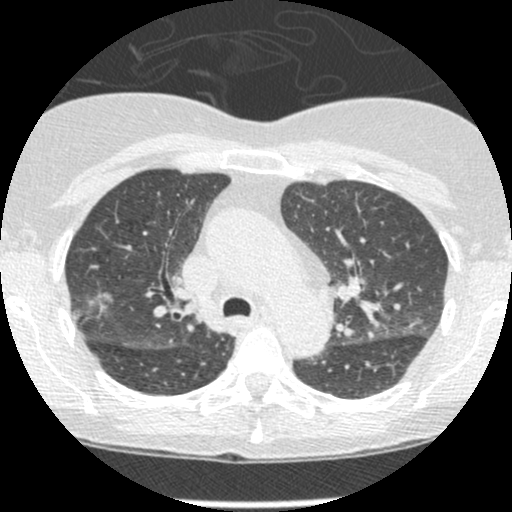
Low-dose screening chest CT, one axial slice. Slice 172 of 238 in the series (ordered by position). Reconstruction kernel STANDARD. Lung window (W 1500 / L -600 HU). 1.25 mm slice thickness. 512 × 512 image matrix.
Structures marked on this image (manually delineated by an expert):
- lesion 1 (tumor, upper lobe of right lung): box from (x=91, y=294) to (x=109, y=310) px